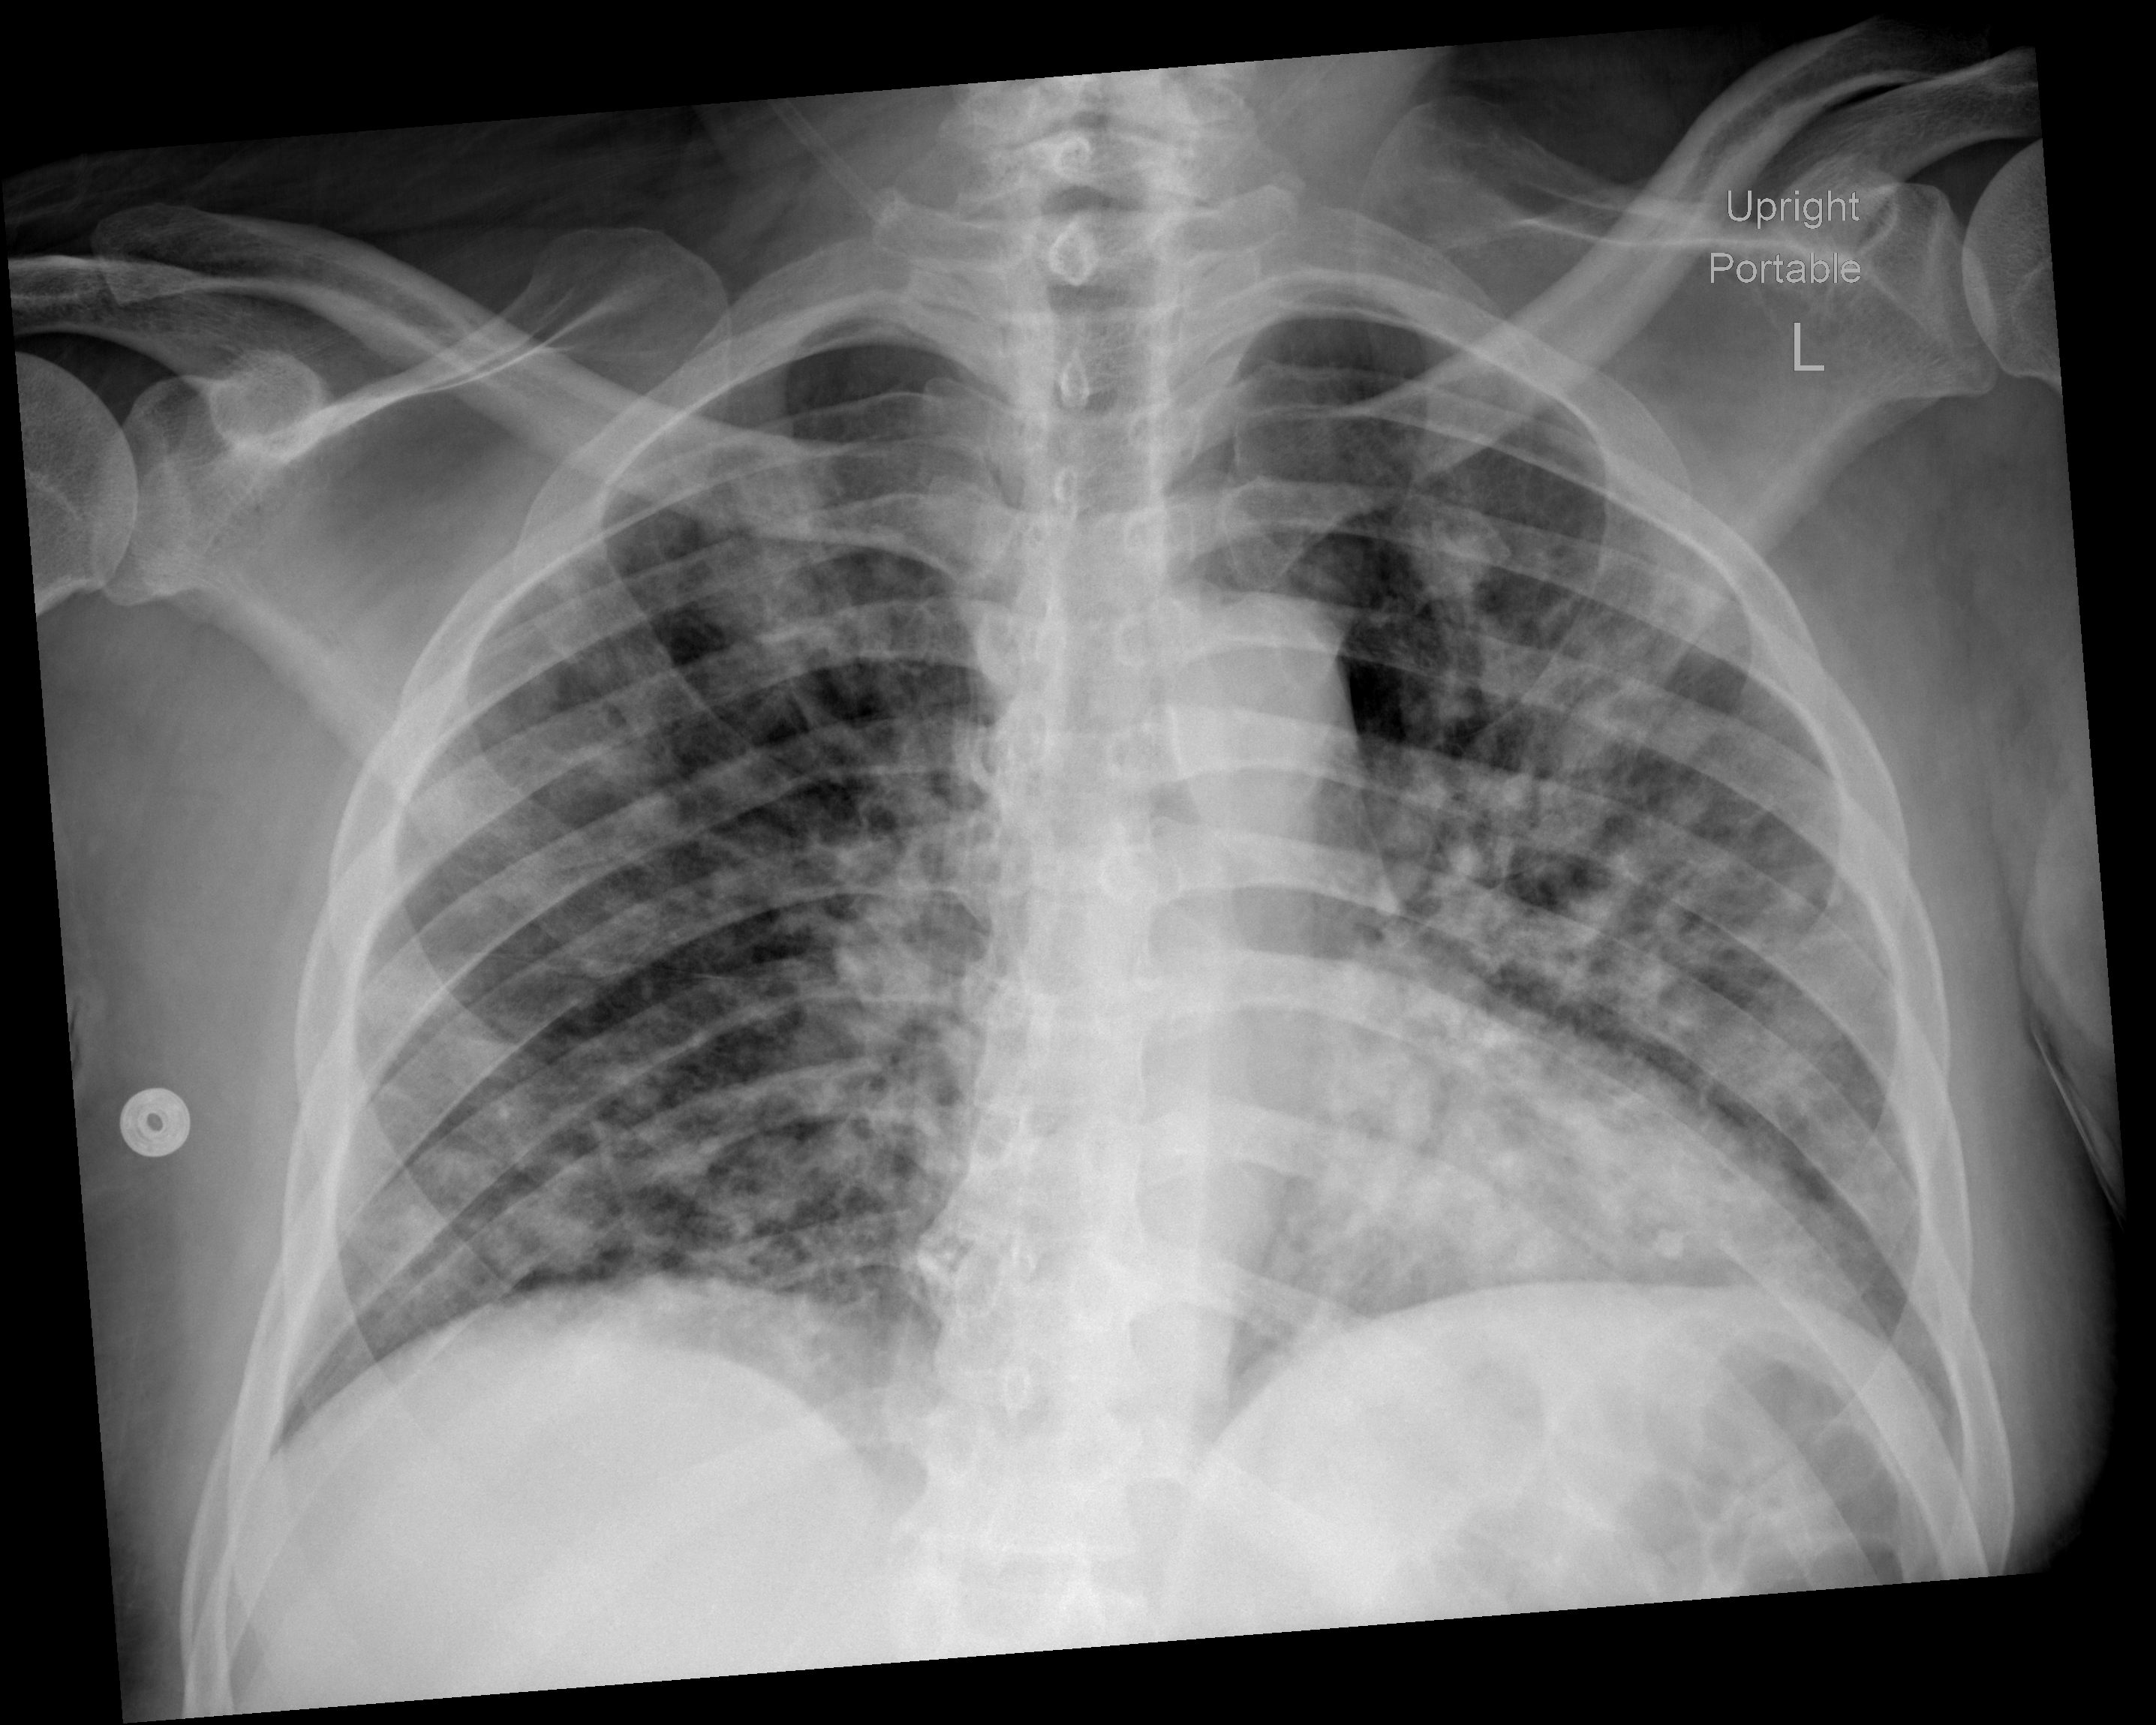
Chest radiograph, AP projection. Male patient, age 55 years; imaged 7 days after the COVID-19 diagnosis.
Key findings recorded by the radiologist: worsened diffuse bilateral mainly peripheral infiltrates involving both lungs.